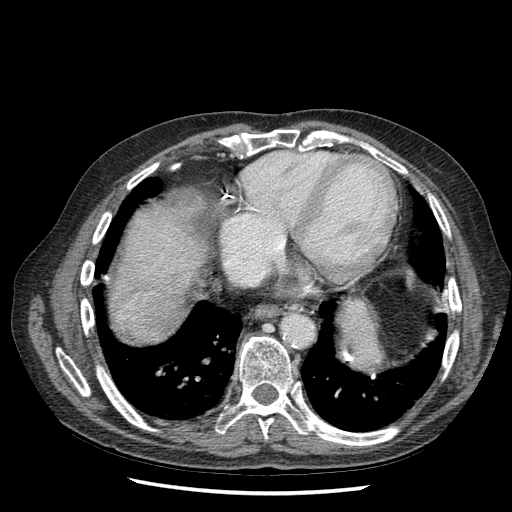
Contrast-enhanced abdominal CT (liver protocol), one axial slice; reconstruction kernel STANDARD; 120 kVp; soft-tissue window (W 400 / L 40 HU); 2.5 mm slice thickness; 512 × 512 image matrix. From the clinical record (not read from this slice): diagnosis: hepatocellular carcinoma (patient treated with transarterial chemoembolisation; whether this scan precedes or follows treatment is not stated here); TNM stage (as recorded): Stage-I; Child-Pugh class: A; tumour differentiation: moderately differentiated; tumour nodularity: uninodular.
Annotated regions visible in this slice (semi-automatically segmented with operator editing):
- liver parenchyma outside the tumour (the mass and vessels are separate outlines, so this box may not span the whole liver): bounding box [x1, y1, x2, y2] px = [134, 208, 190, 326]
- mass: [135, 293, 174, 328]